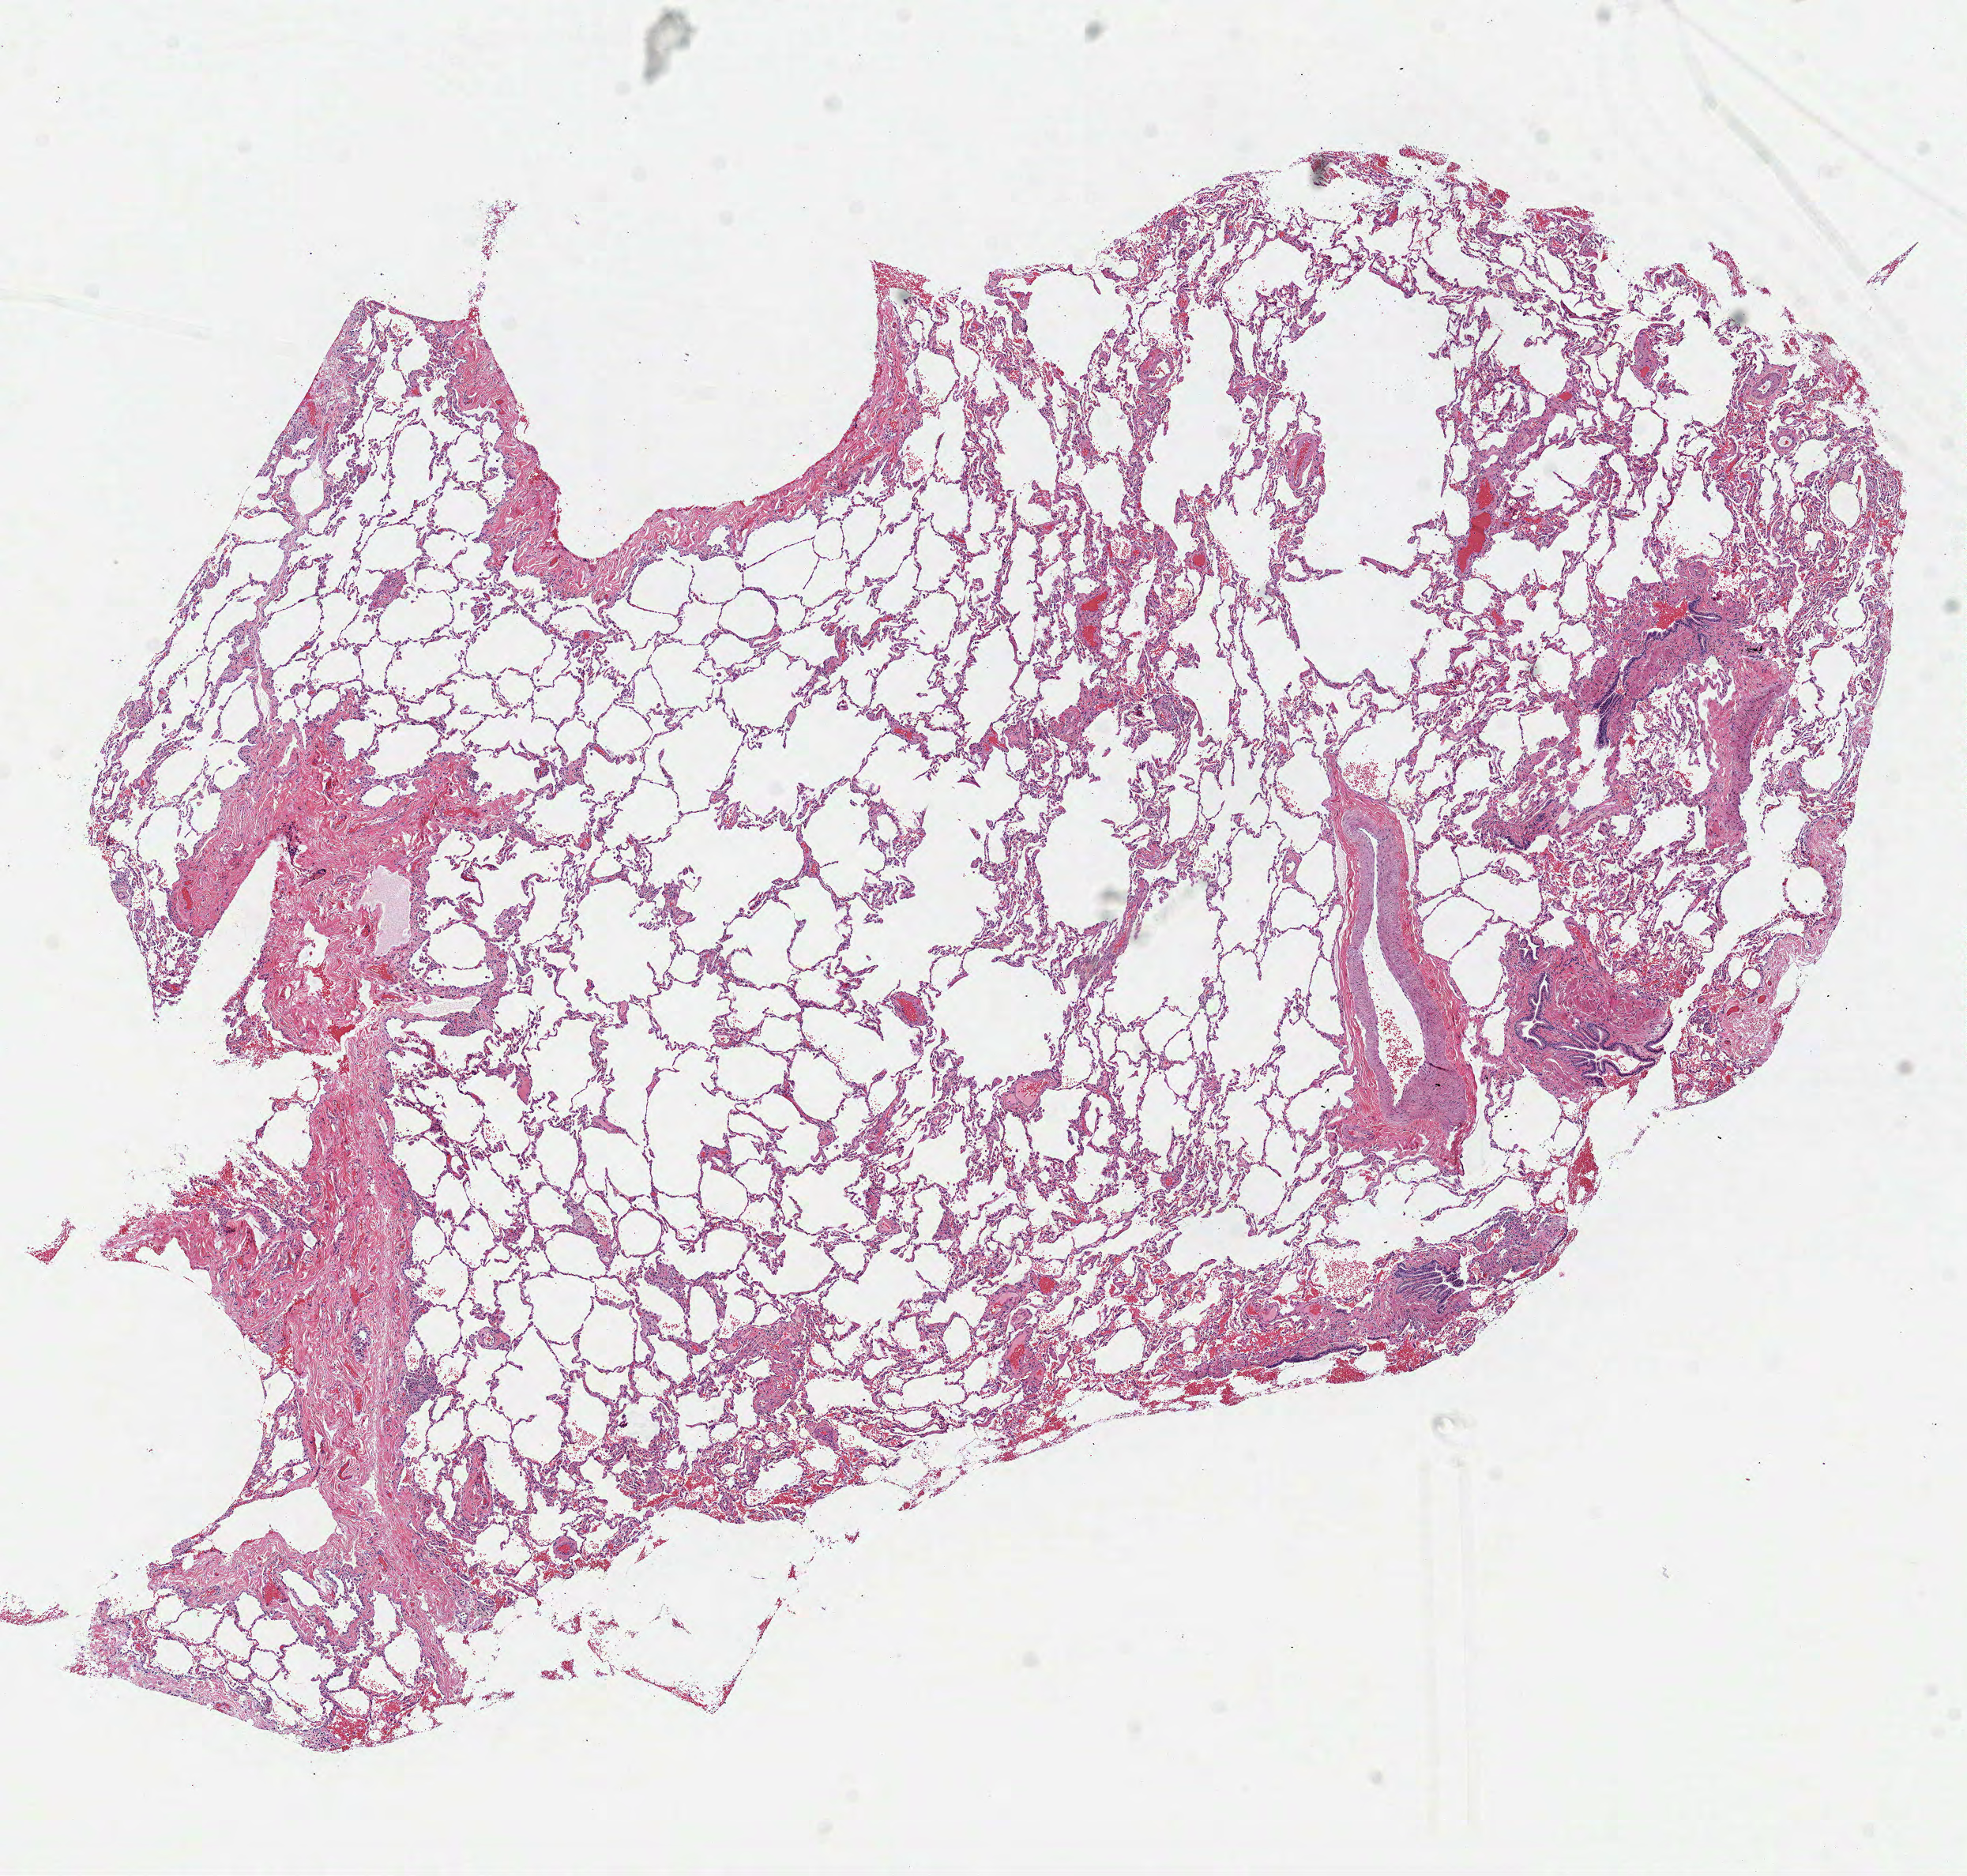
Digitized Hematoxylin and eosin (H&E) stained tissue section (whole slide), a low-resolution overview of the entire scanned area, about 10.0 x 9.6 mm; frozen section; sample: solid tissue normal (non-tumour tissue), lung. Male patient; age at initial diagnosis 60 years.
This section: solid tissue normal sample (biorepository sample class). Patient diagnosis: Mucinous adenocarcinoma (lower lobe, lung).